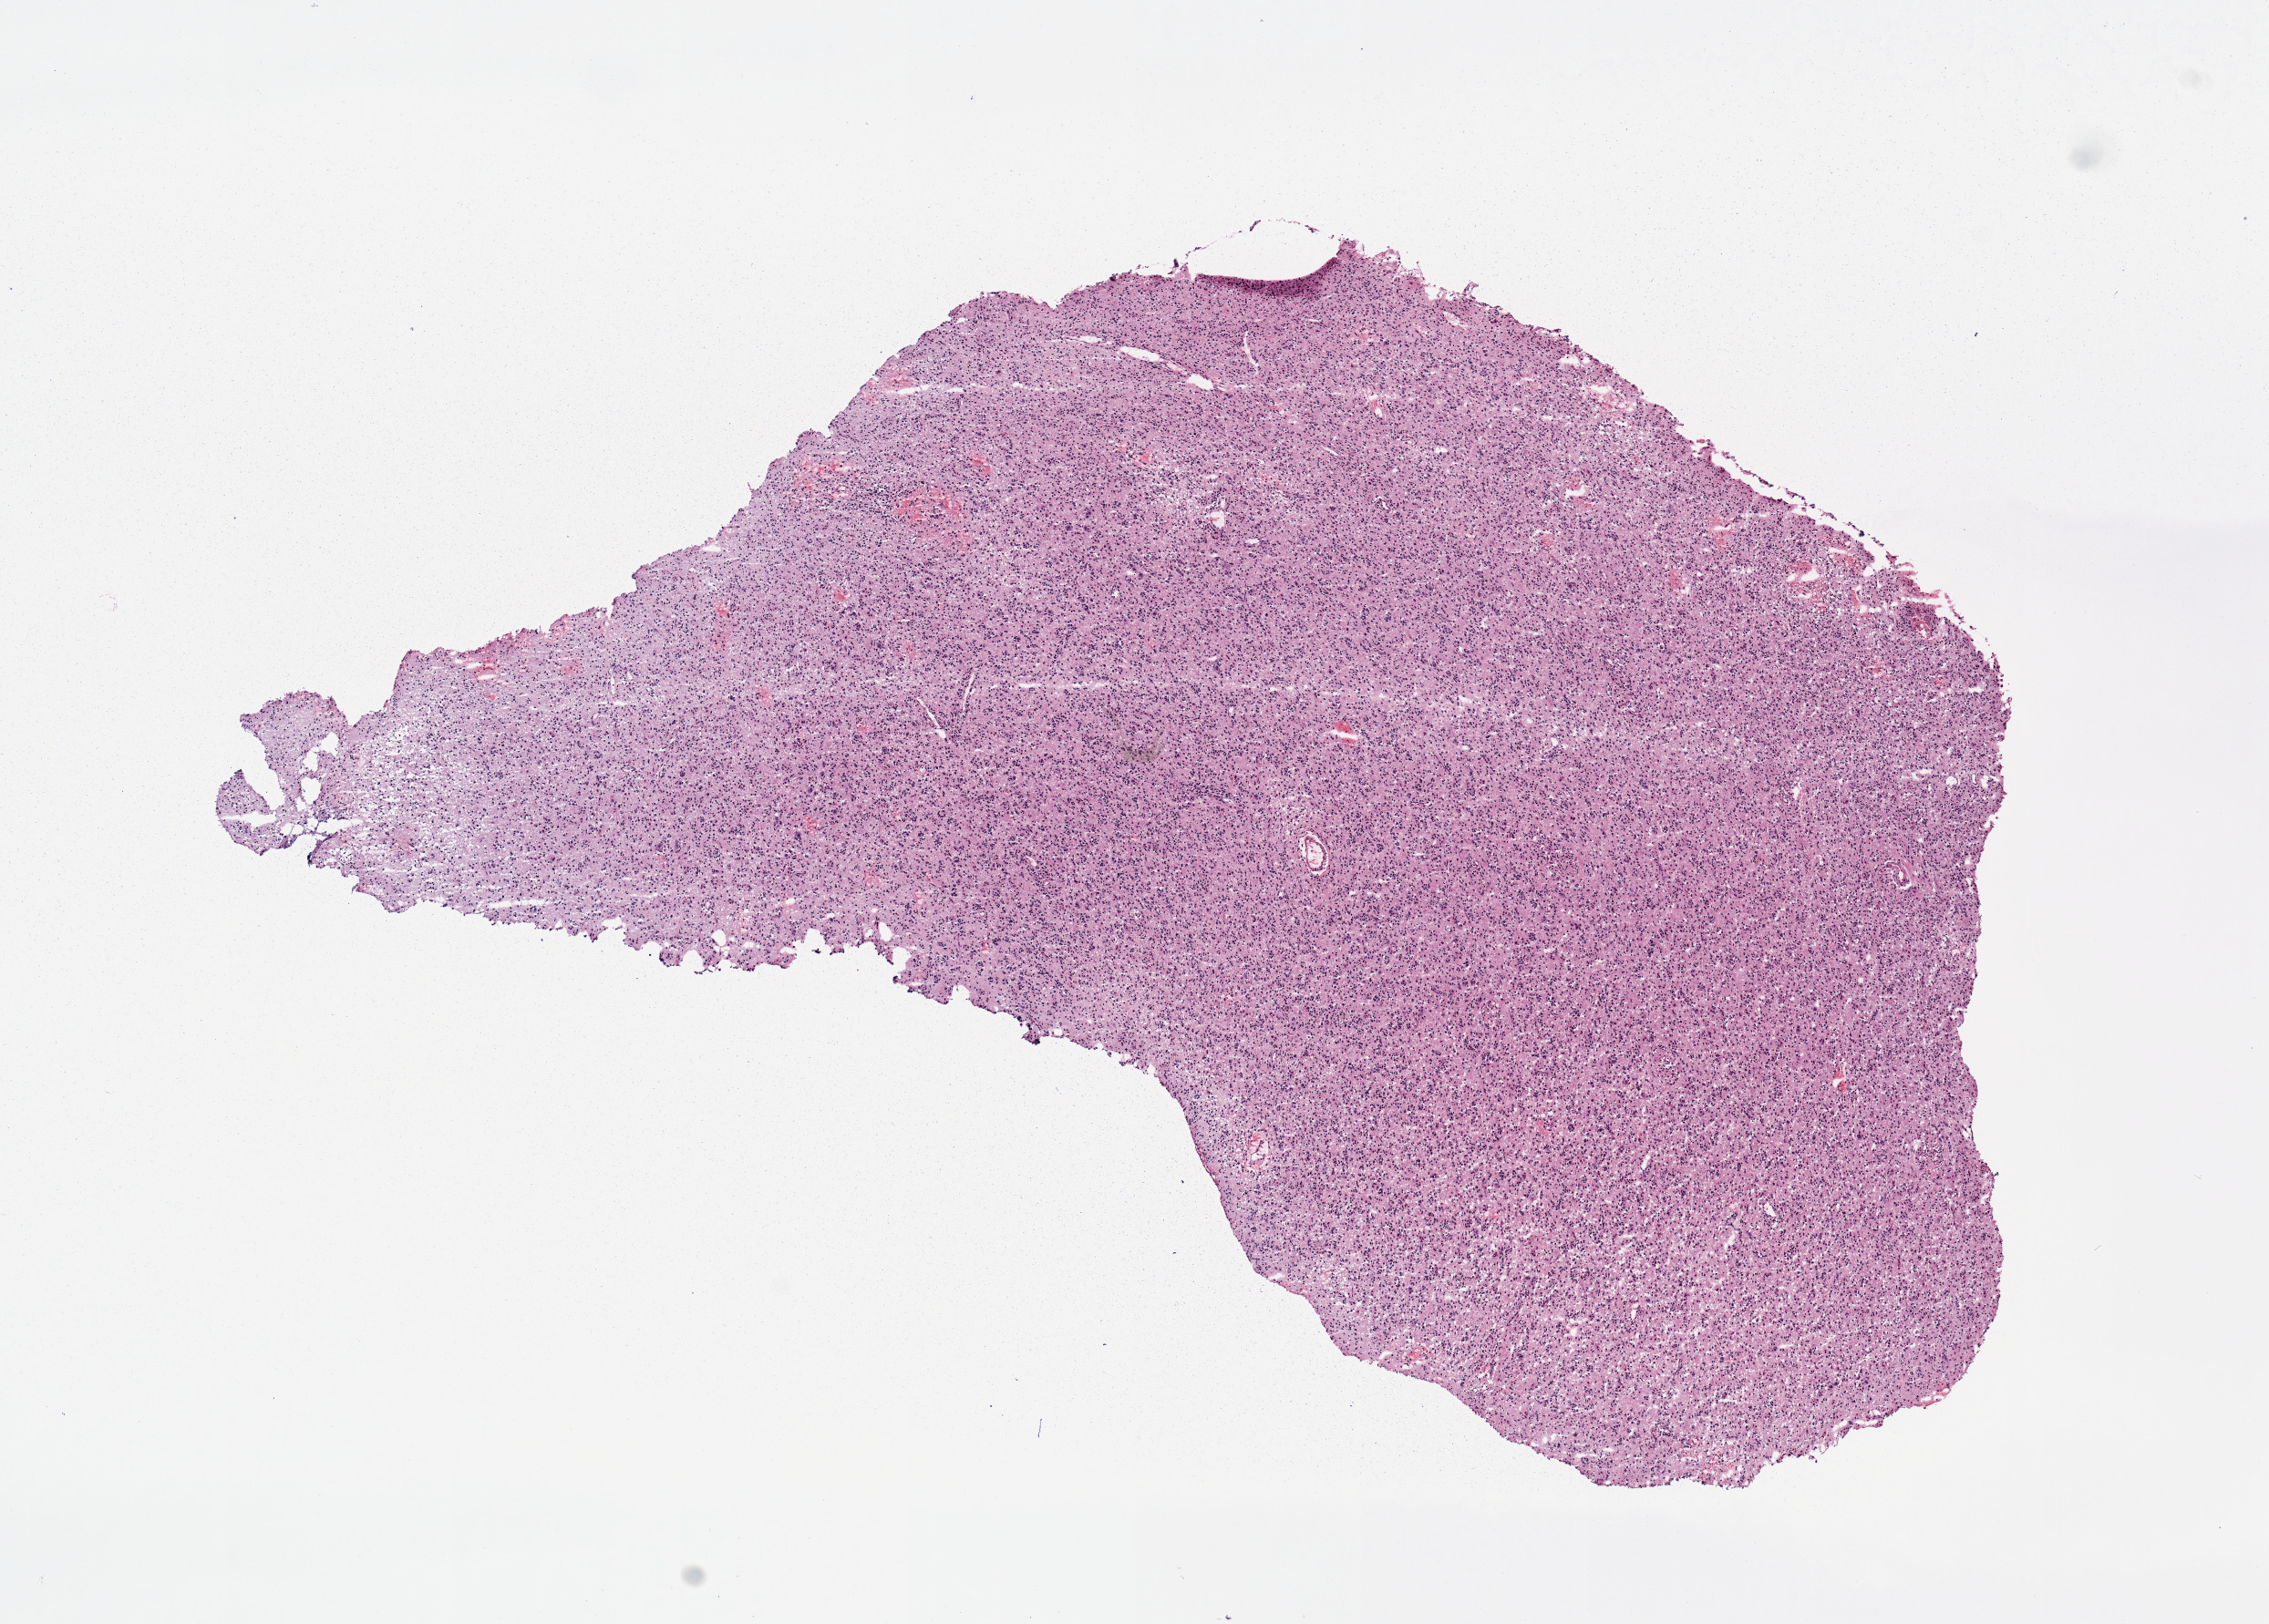
Digitized H&E tissue section (whole slide) — a low-resolution overview of the entire scanned area, about 9.8 x 7.0 mm (acquisition: 20x scan); tumour tissue sample, brain. Patient: male, age 51 years.
Primary tumour site (as recorded): frontal lobe. Patient diagnosis (cohort enrolment): glioblastoma multiforme (brain).